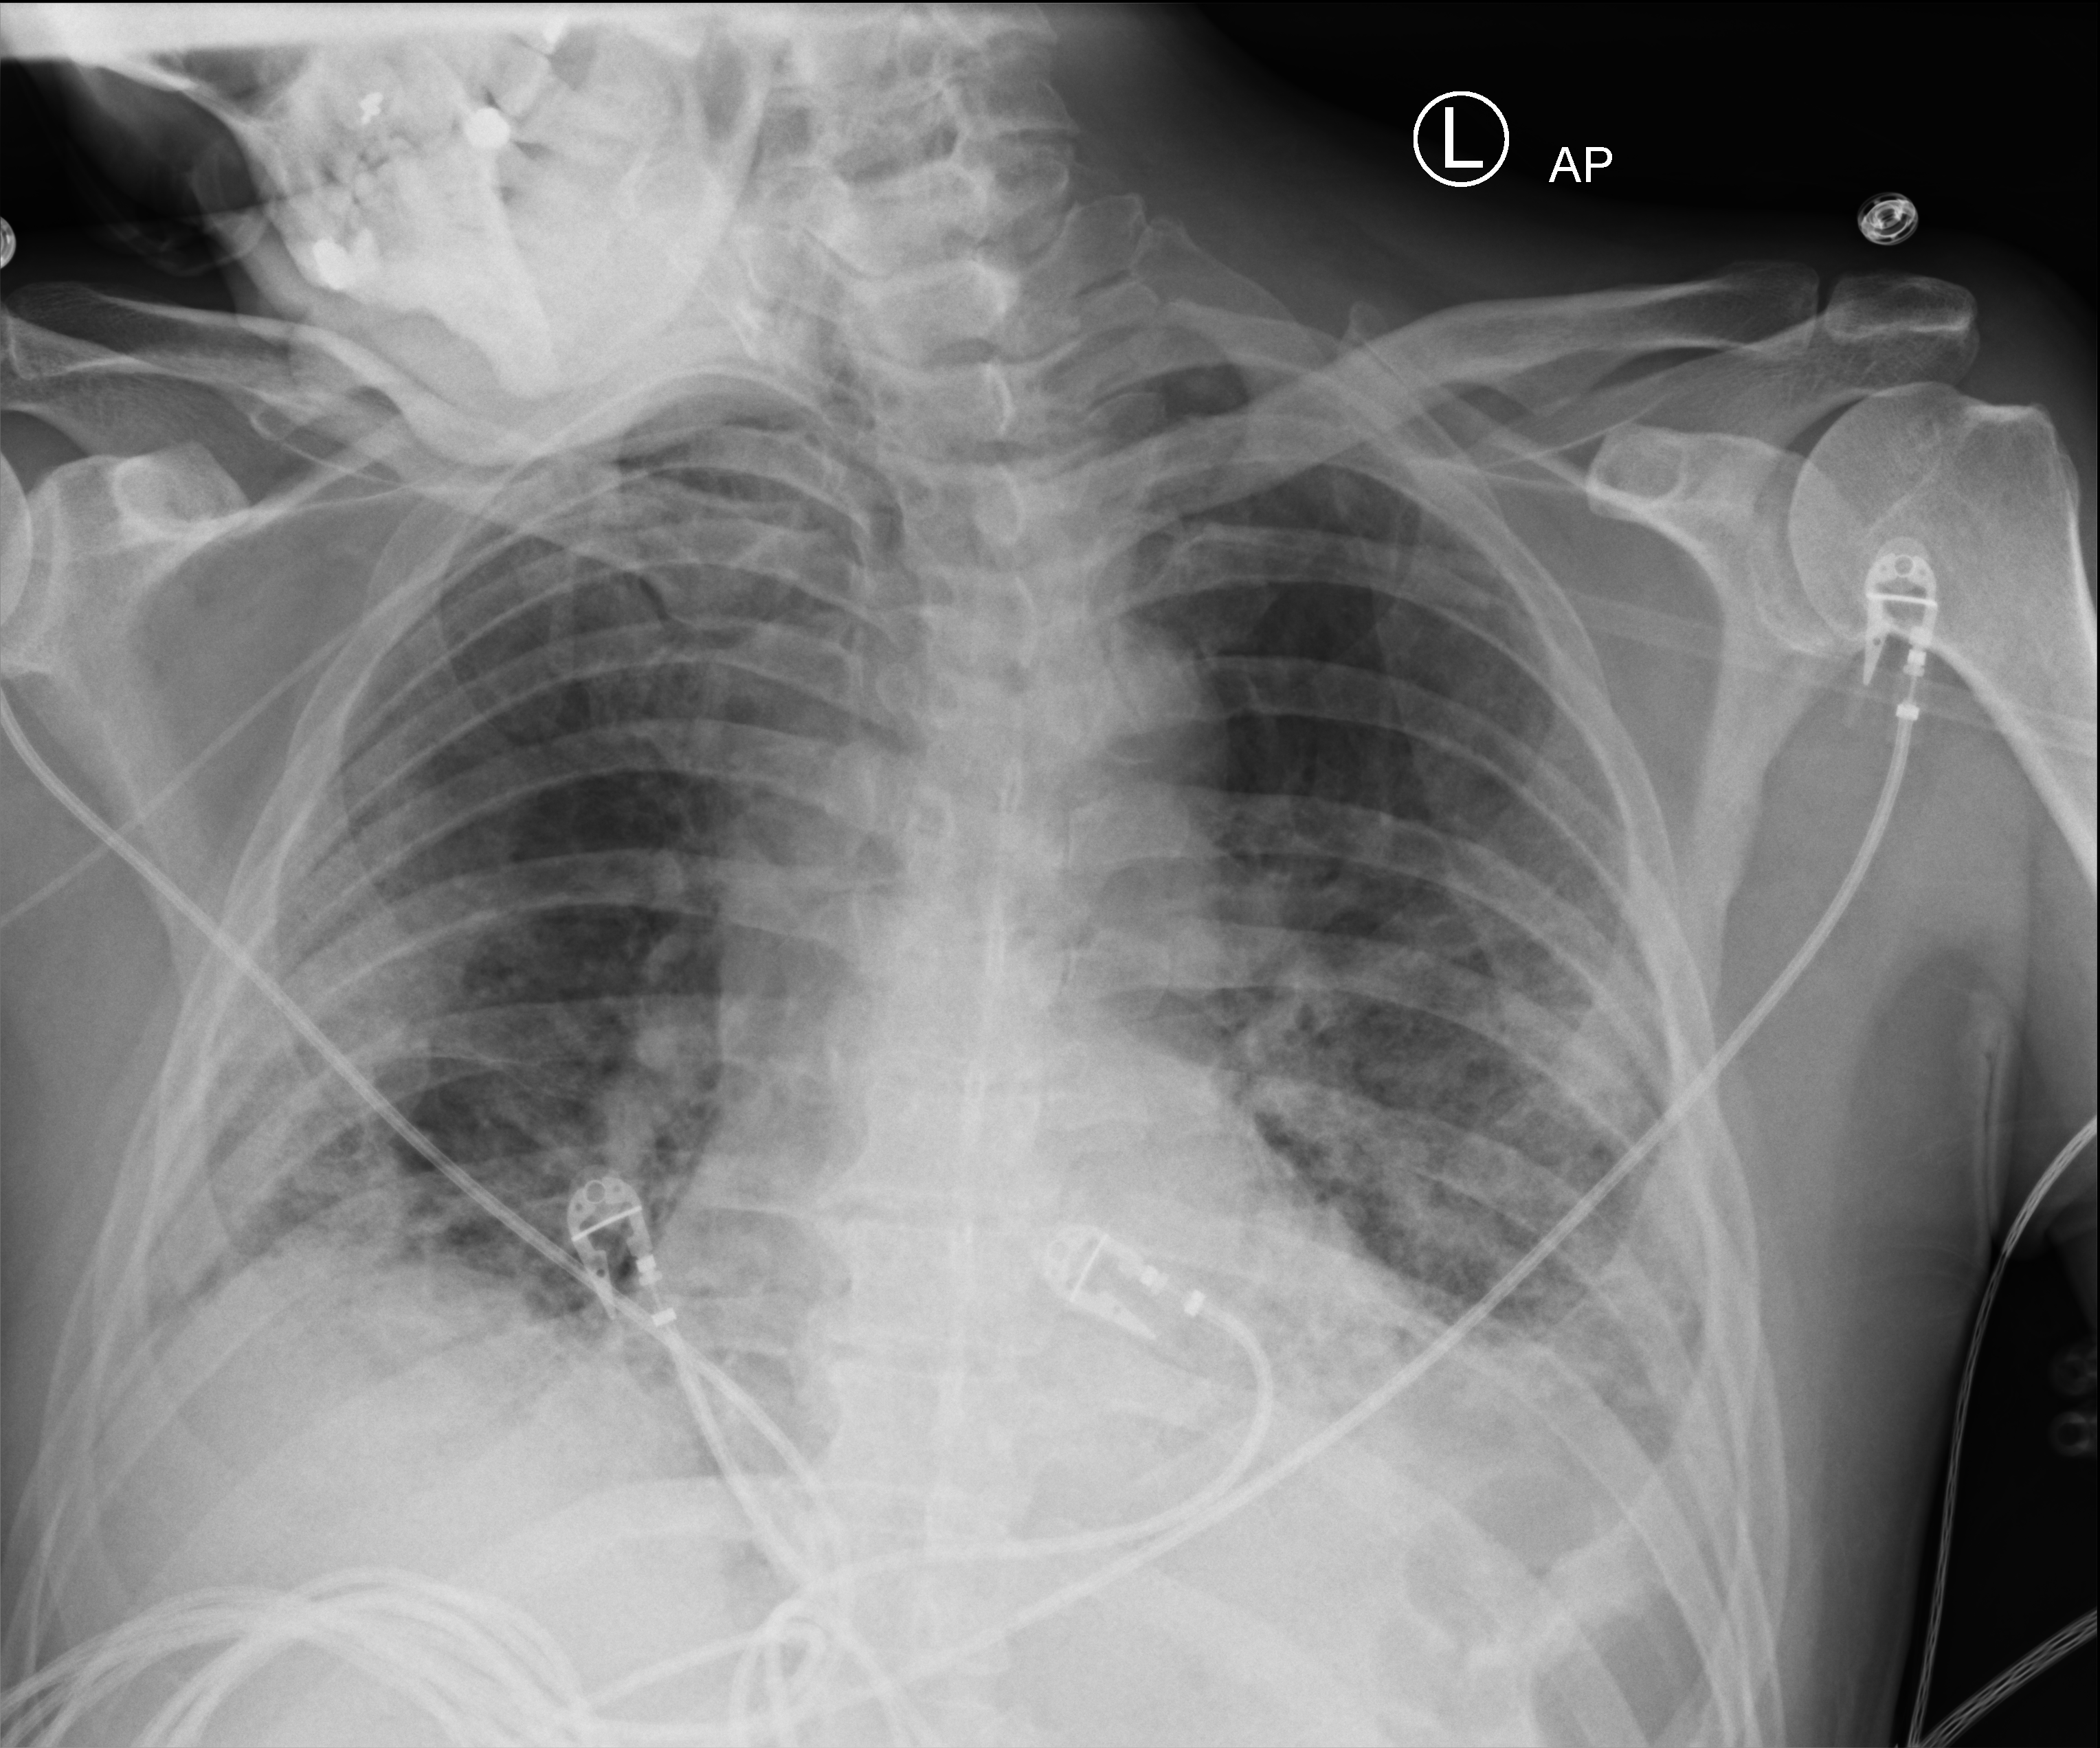
Bedside chest radiograph (computed radiography), anteroposterior (AP) projection. Patient hospitalised with COVID-19; male, aged 60–74 years.
Admission-level facts for this patient (not findings on this image; timing relative to this image not recorded):
- COPD (admission record): no
- length of hospital stay: 26 days